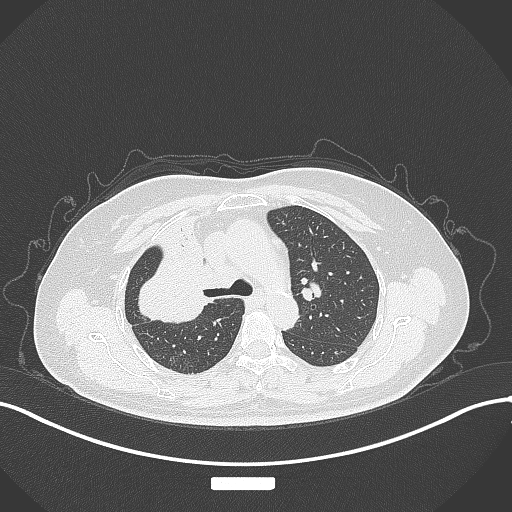
Chest CT, one axial slice. Position 216 of 309 along the scan axis. Lung window (W 1500 / L -600 HU). 1 mm slice thickness. 512 × 512 image matrix, field of view 400 × 400 mm. Patient: female, 60 years. Case-level facts recorded for this patient, not image findings: clinical TNM (as recorded): T3 N1 M1.
Structures marked on this image (rectangle marked by the reading radiologist):
- lung tumour (recorded histology: adenocarcinoma): bounding box (x1, y1, x2, y2) in pixels: (130, 240, 217, 332)